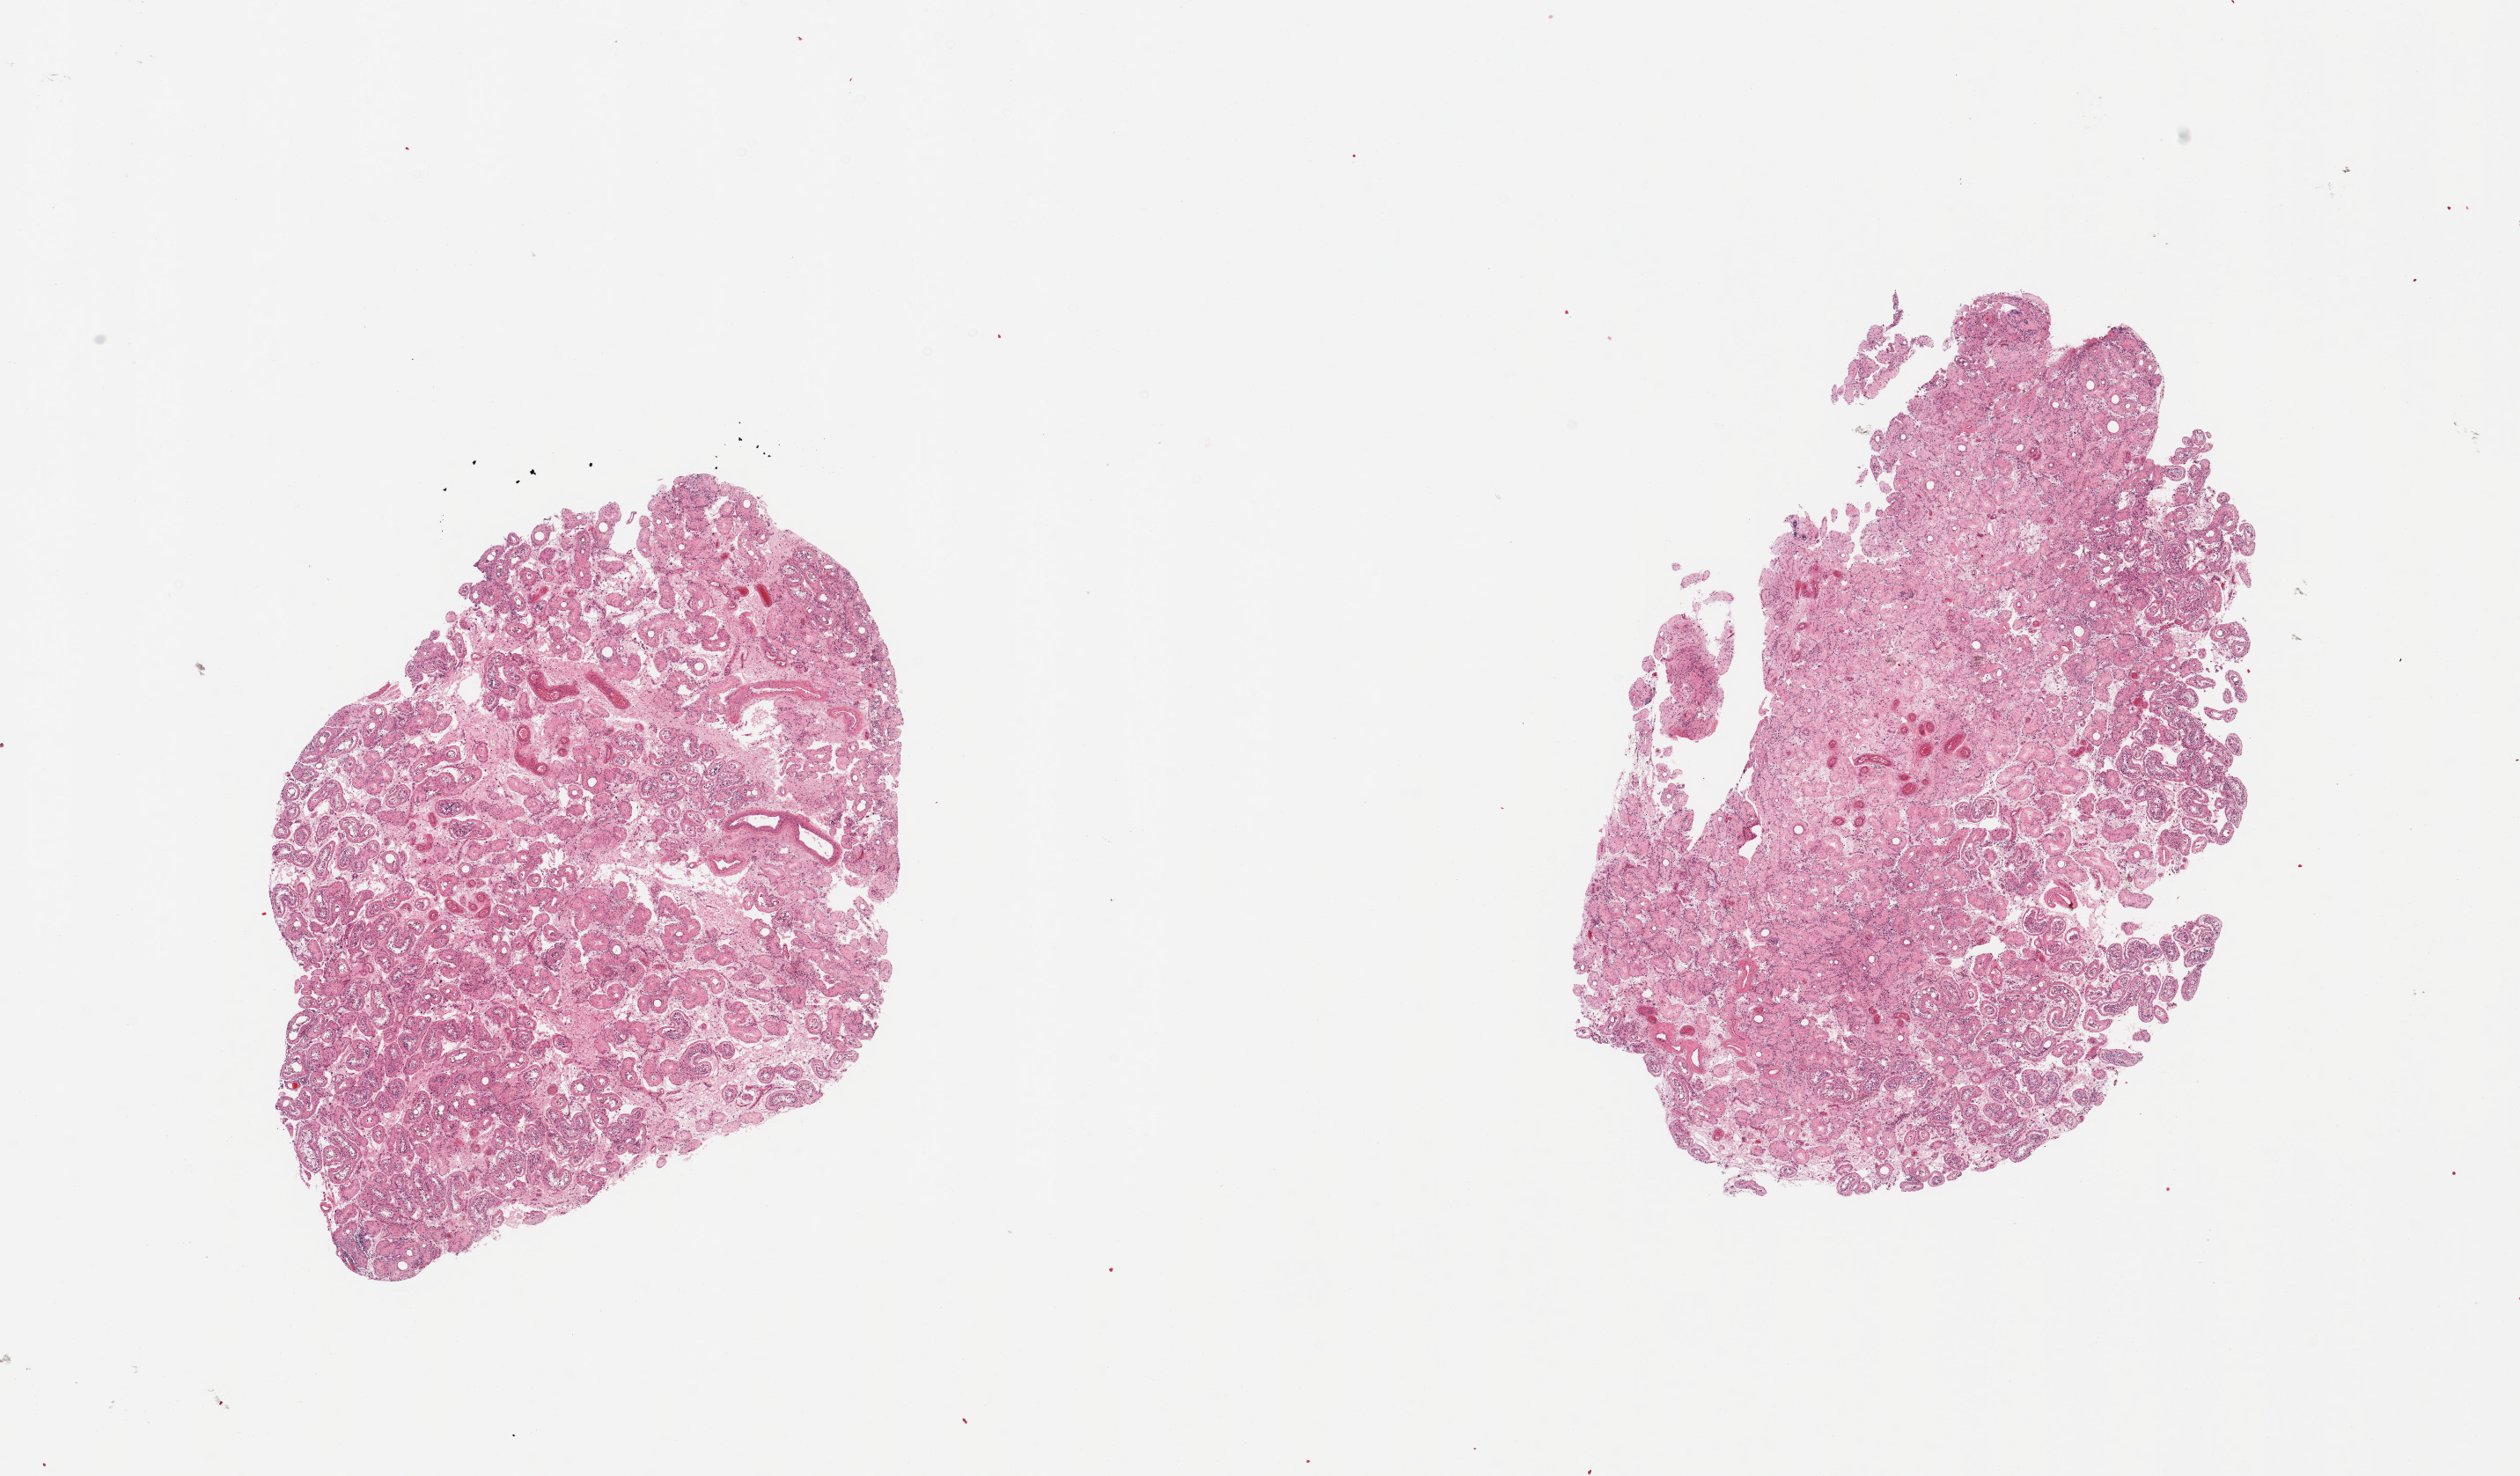
Hematoxylin and eosin (H&E) whole-slide image — a low-resolution overview of the entire scanned area, about 22.6 x 13.3 mm (acquisition: 20x scan). PAXgene-fixed, paraffin-embedded tissue. Target tissue: testis. Donor tissue sample. Donor sex: male.
Pathologist's review note for this sample: 2 pieces; 80% fibrotic & sclerotic tubules with no spermatogenesis; 20% focus of intact tubules with incomplete spermatogenesis; no Leydig cell hyperplasia.